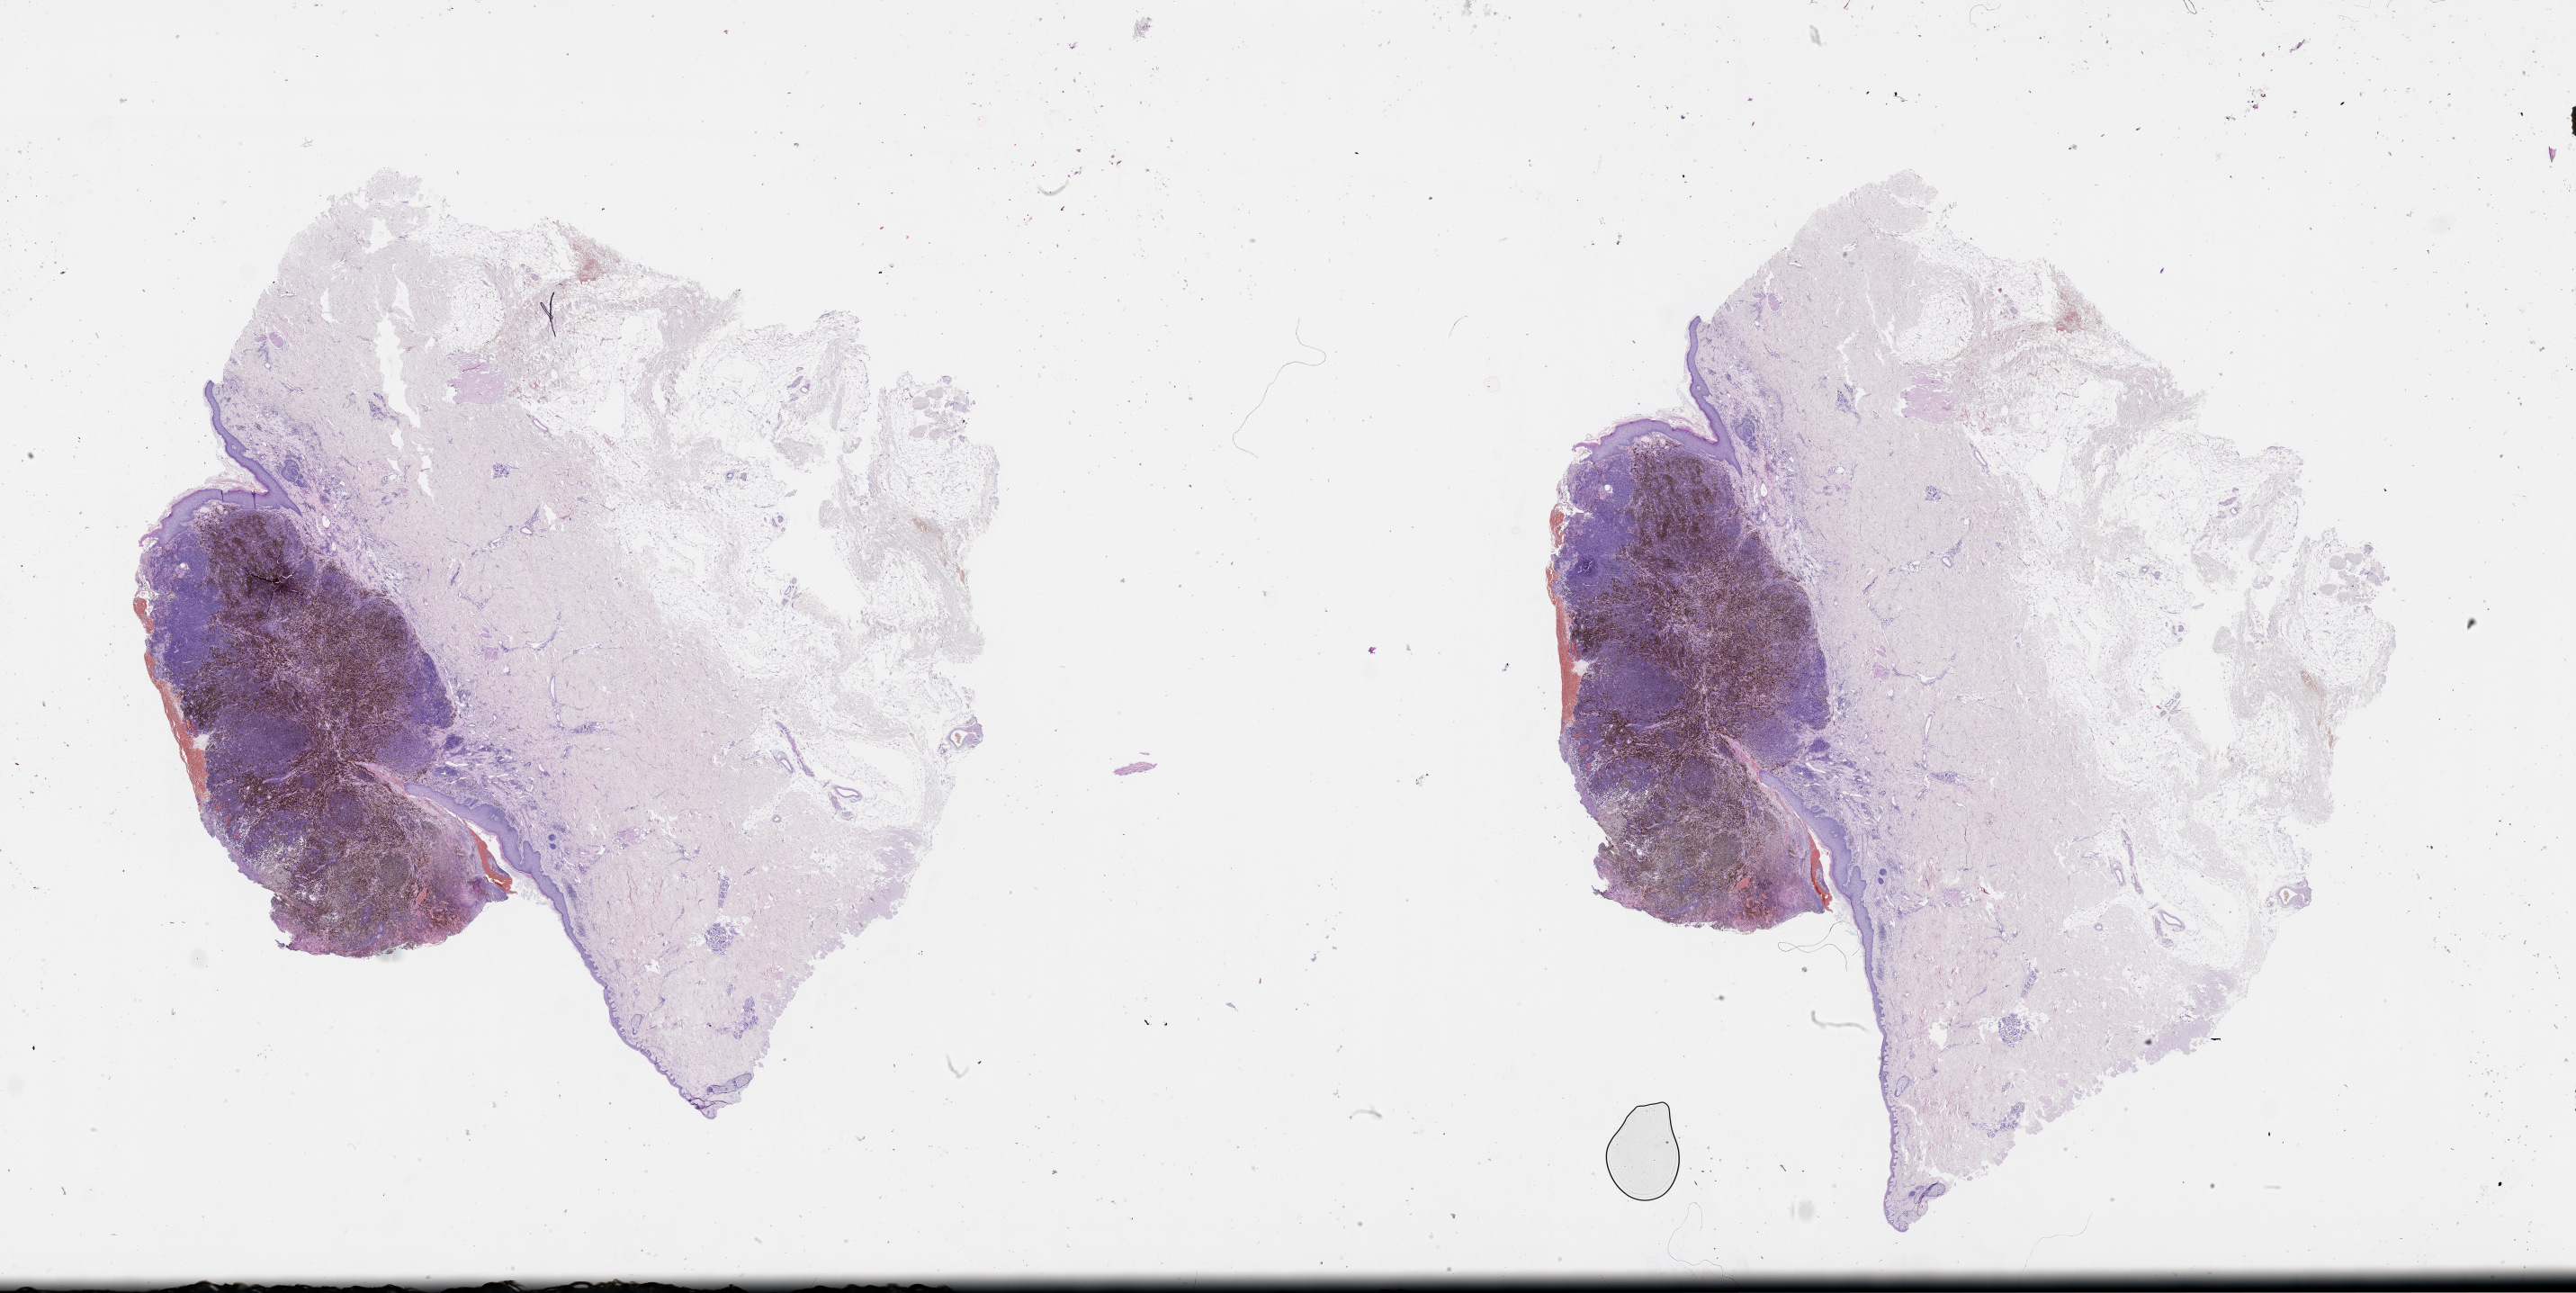
Whole-slide histology image, H&E-stained — whole scanned area (about 46.1 x 23.1 mm, slide scanned at 20x) shown as a low-resolution overview. 82-year-old male patient.
• patient diagnosis: Malignant melanoma, NOS